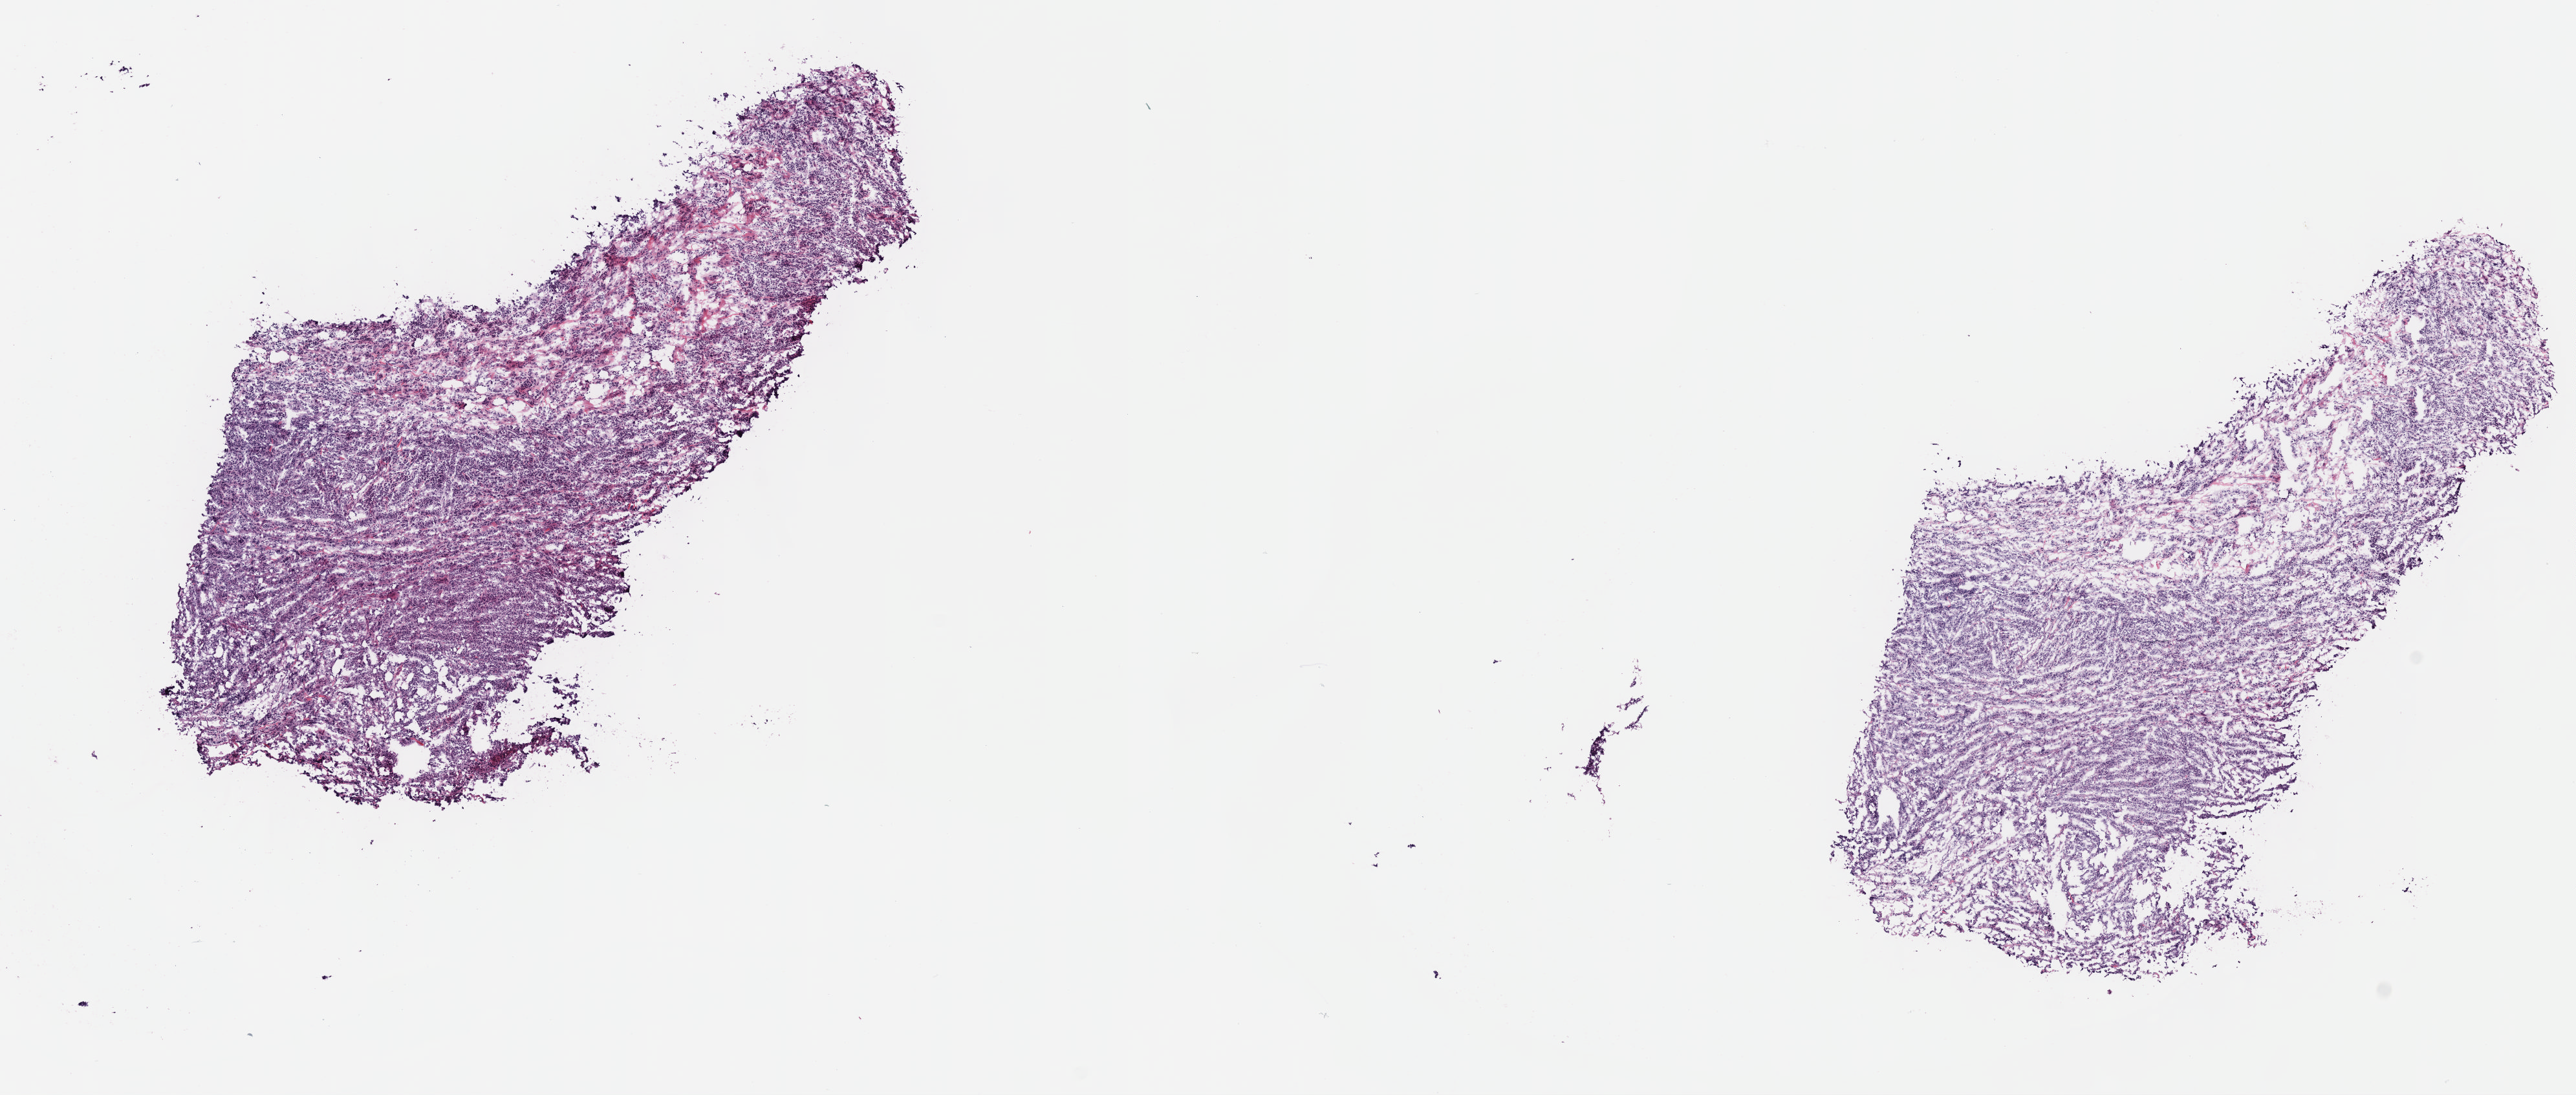
H&E whole-slide image, a low-resolution overview of the entire scanned area, about 16.1 x 6.8 mm (acquisition: 40x scan). Frozen section from the top of the tissue portion. Primary tumour sample from the lymphoid tissue. Patient: female, age at initial diagnosis 61 years. Composition of this section per pathologist review: tumour cells 70%, tumour nuclei 80%, normal cells 0%, stromal cells 20%, necrosis 10%. Infiltration values recorded for this section: lymphocyte infiltration 80%, monocyte infiltration 10%, neutrophil infiltration 5%.
Diagnosis: Diffuse large B-cell lymphoma, NOS (specified parts of peritoneum).